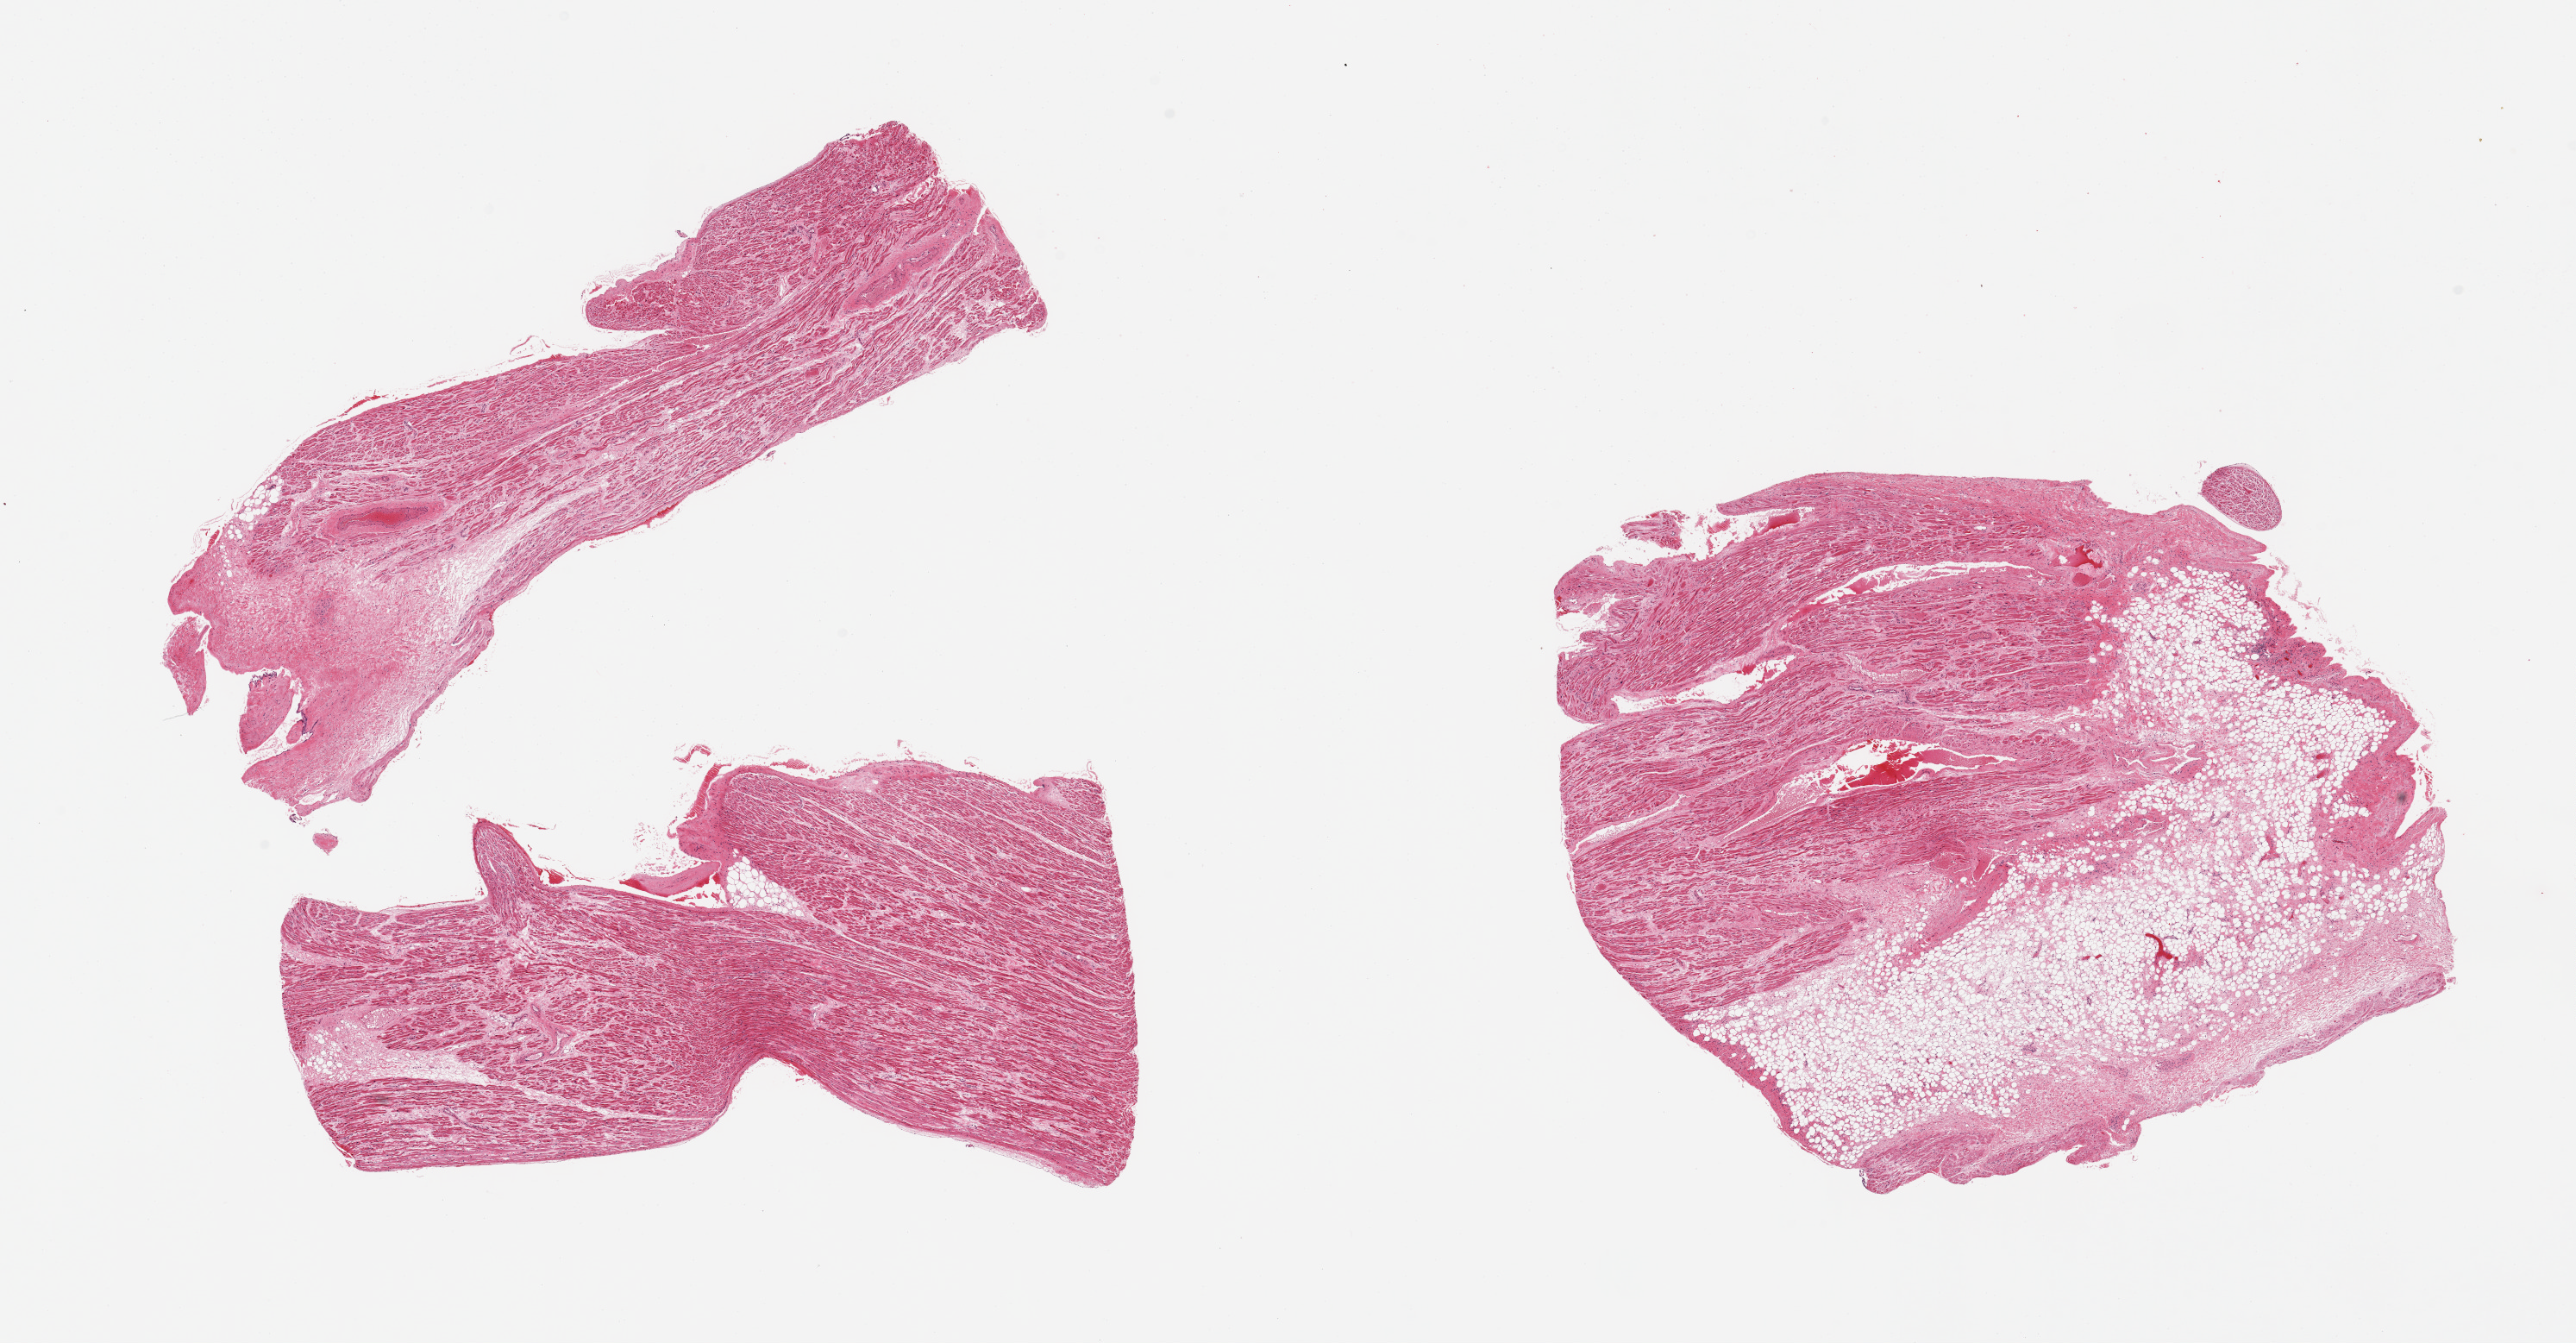
Digitized hematoxylin and eosin (H&E)-stained section — shown as a low-resolution overview of the whole scanned area (about 23.6 x 12.3 mm), PAXgene-fixed, paraffin-embedded tissue, target tissue: auricular appendage, tissue donor sample. Male donor.
Review note (as recorded): 2 pieces; fibromuscular tissue; one piece with up to 50% internal fat.